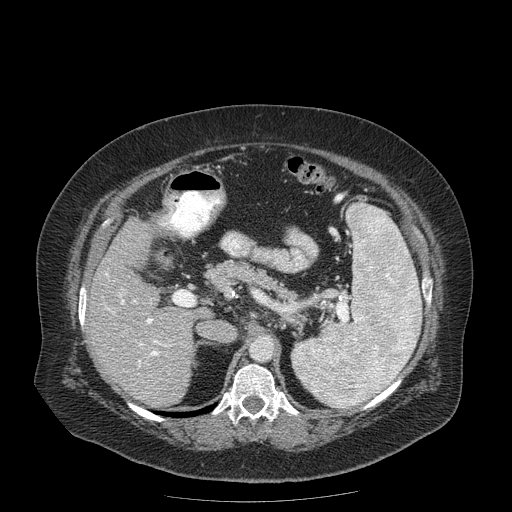
Contrast-enhanced abdominal CT (liver protocol), one axial slice. Position 99 of 204 along the scan axis. Reconstruction kernel STANDARD. Soft-tissue window (W 400 / L 40 HU). 2.5 mm slice thickness. 512 × 512 image matrix, field of view 440 × 440 mm. Case-level facts recorded for this patient, not image findings: diagnosis: hepatocellular carcinoma (patient treated with transarterial chemoembolisation; whether this scan precedes or follows treatment is not stated here); TNM stage (as recorded): Stage-IIIB; Child-Pugh class: A; tumour differentiation: well differentiated; tumour nodularity: uninodular.
Structures marked on this image (semi-automatically segmented with operator editing):
- liver parenchyma outside the tumour (the mass and vessels are separate outlines, so this box may not span the whole liver): bounding box [x1, y1, x2, y2] px = [90, 216, 196, 408]
- liver vessels: [105, 273, 171, 367]